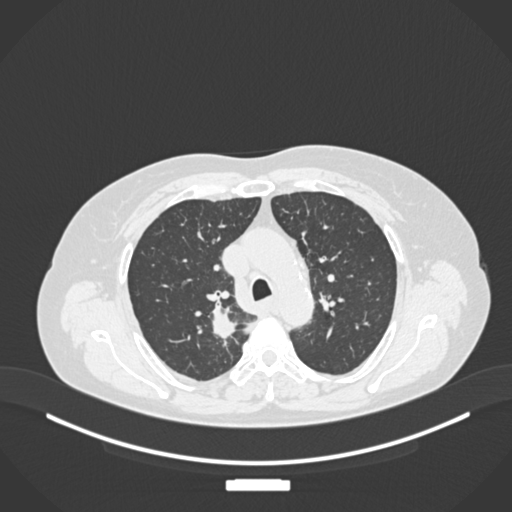
Chest CT, one axial slice; slice 182 of 237 in the series (ordered by position); lung window (W 1500 / L -600 HU); 512 × 512 image matrix, field of view 400 × 400 mm. Patient: female, 62 years. Case-level facts recorded for this patient, not image findings: clinical TNM (as recorded): T1c N1 M0.
Annotated regions visible in this slice (bounding box drawn by a radiologist):
- lung tumour (recorded histology: squamous cell carcinoma): bounding box <207,295,242,344> (left, top, right, bottom; pixels)